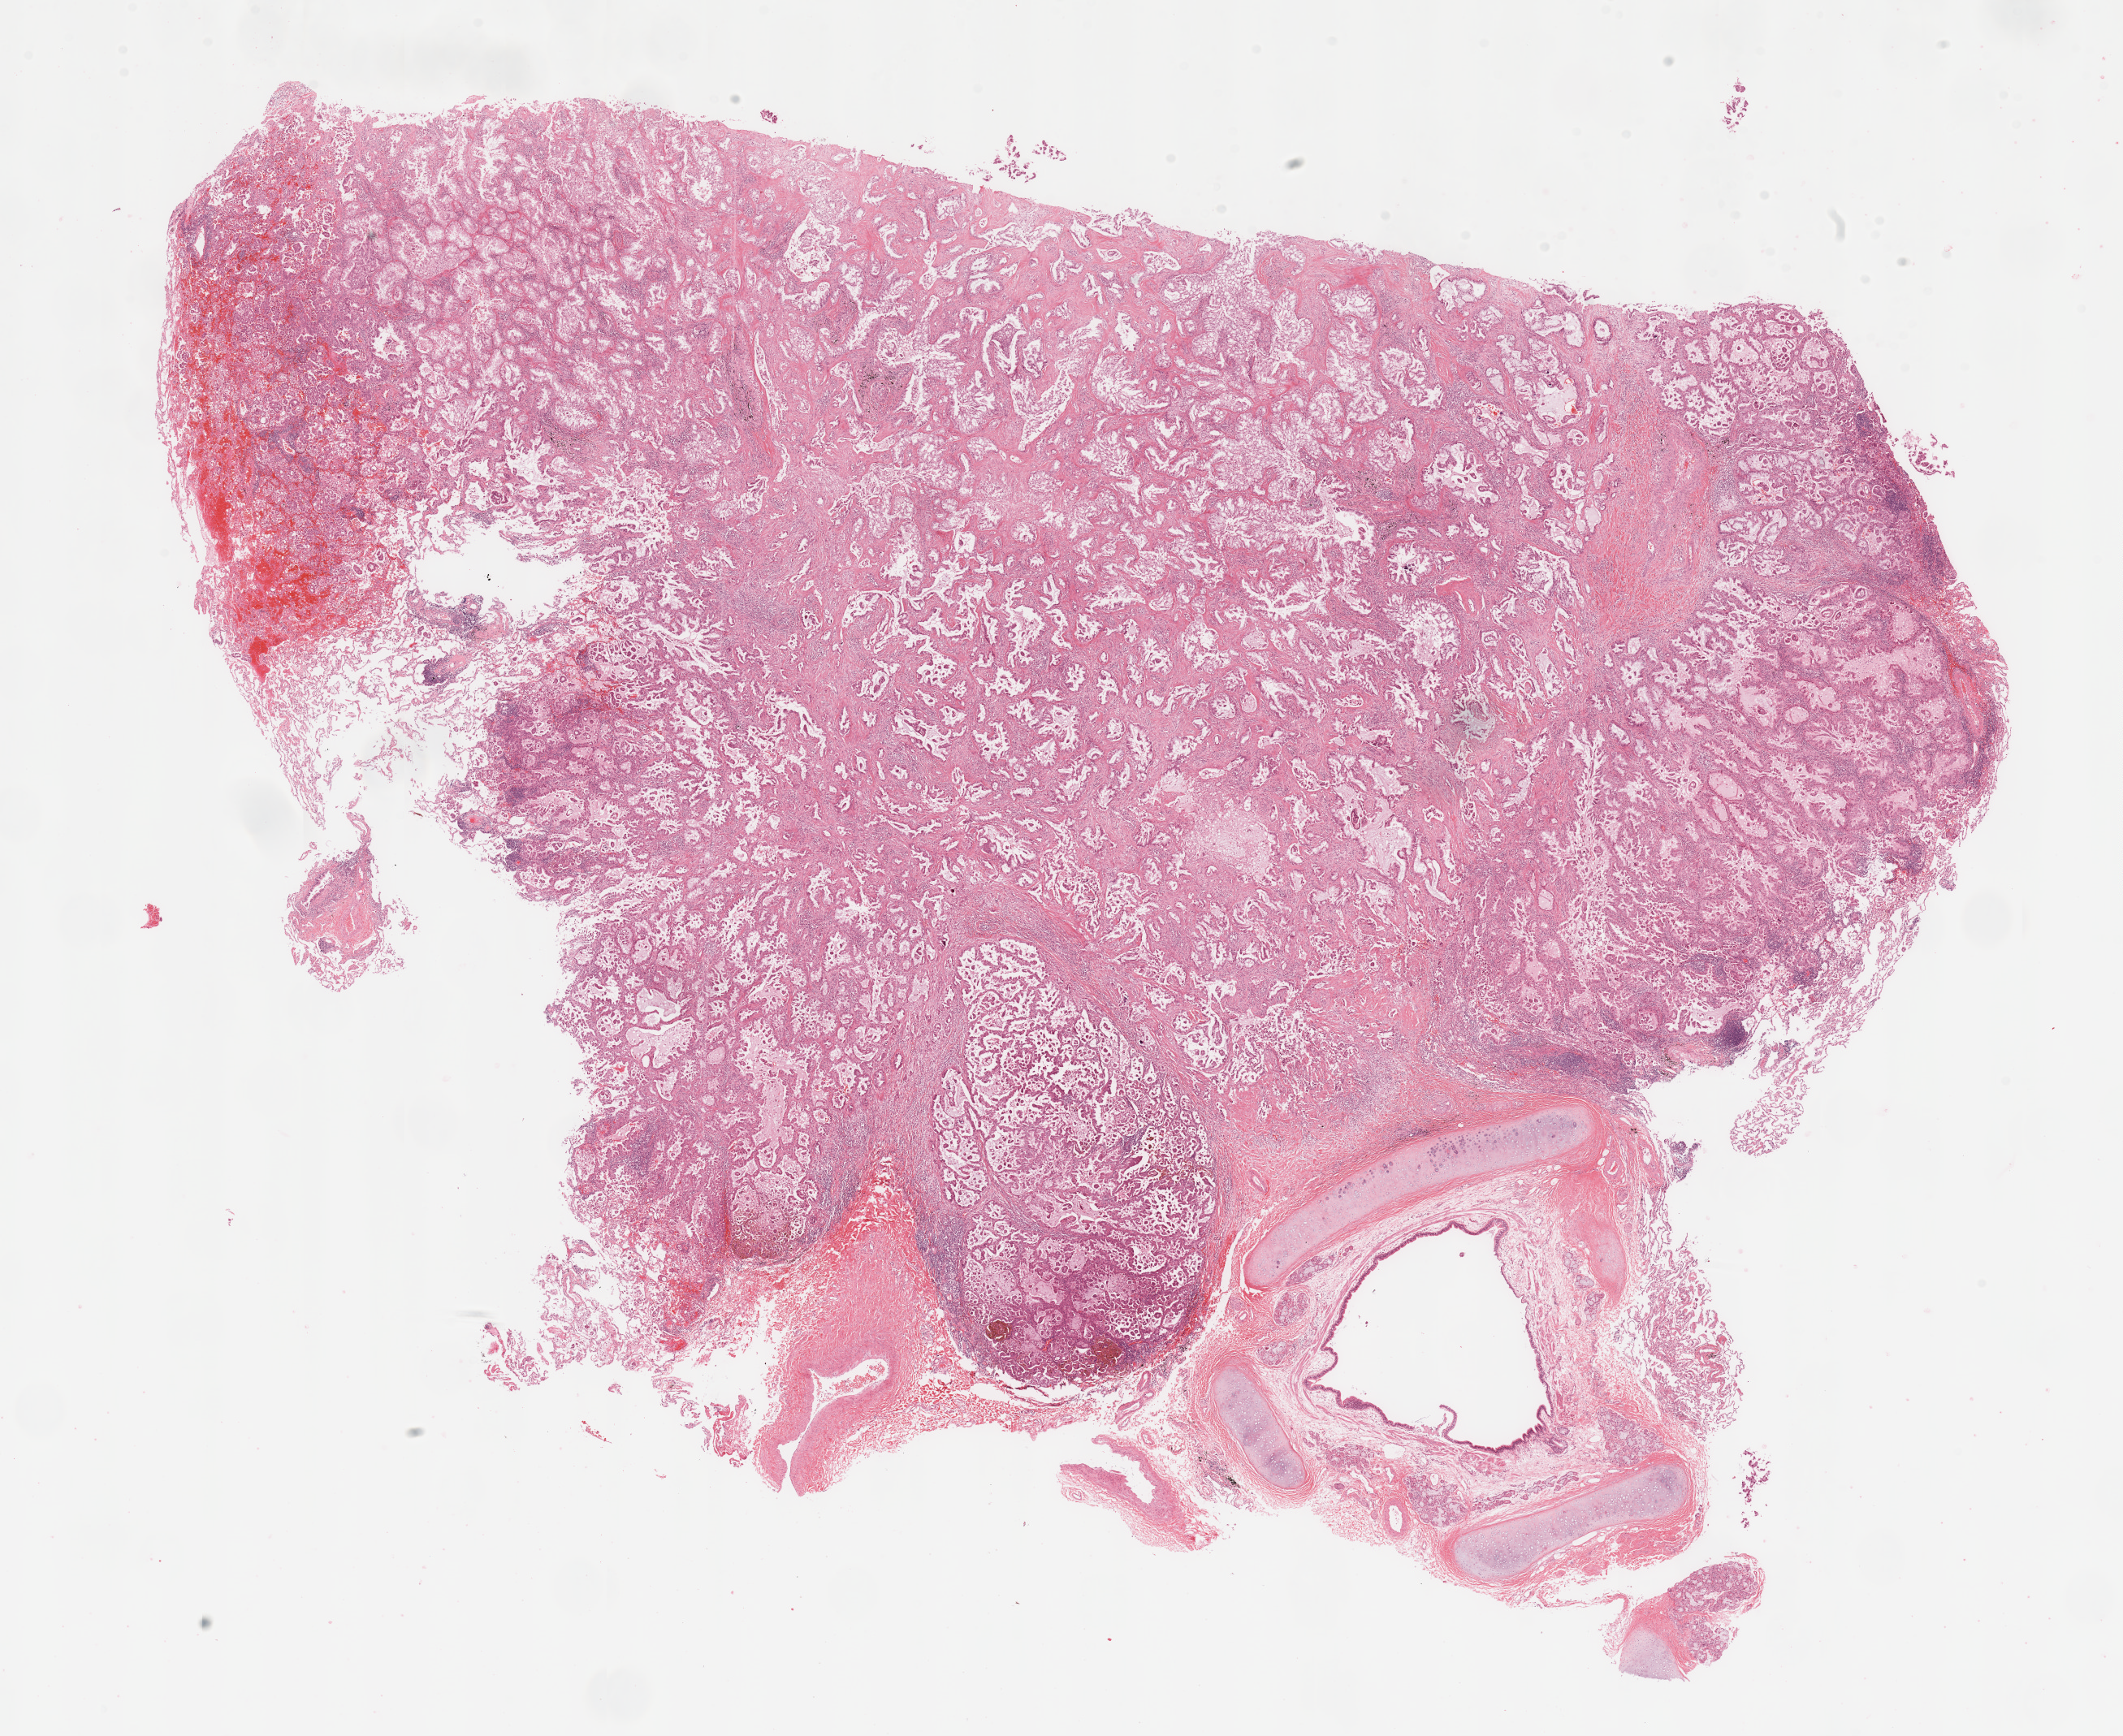
Whole-slide histology image, H&E — shown as a low-resolution overview of the whole scanned area (about 20.7 x 16.9 mm); lung, tumour tissue. 48-year-old female patient. Histologic grade: G2 (moderately differentiated).
* AJCC pathologic stage: IA
* primary tumour site (as recorded): right lower lobe
* diagnosis: Adenocarcinoma, NOS